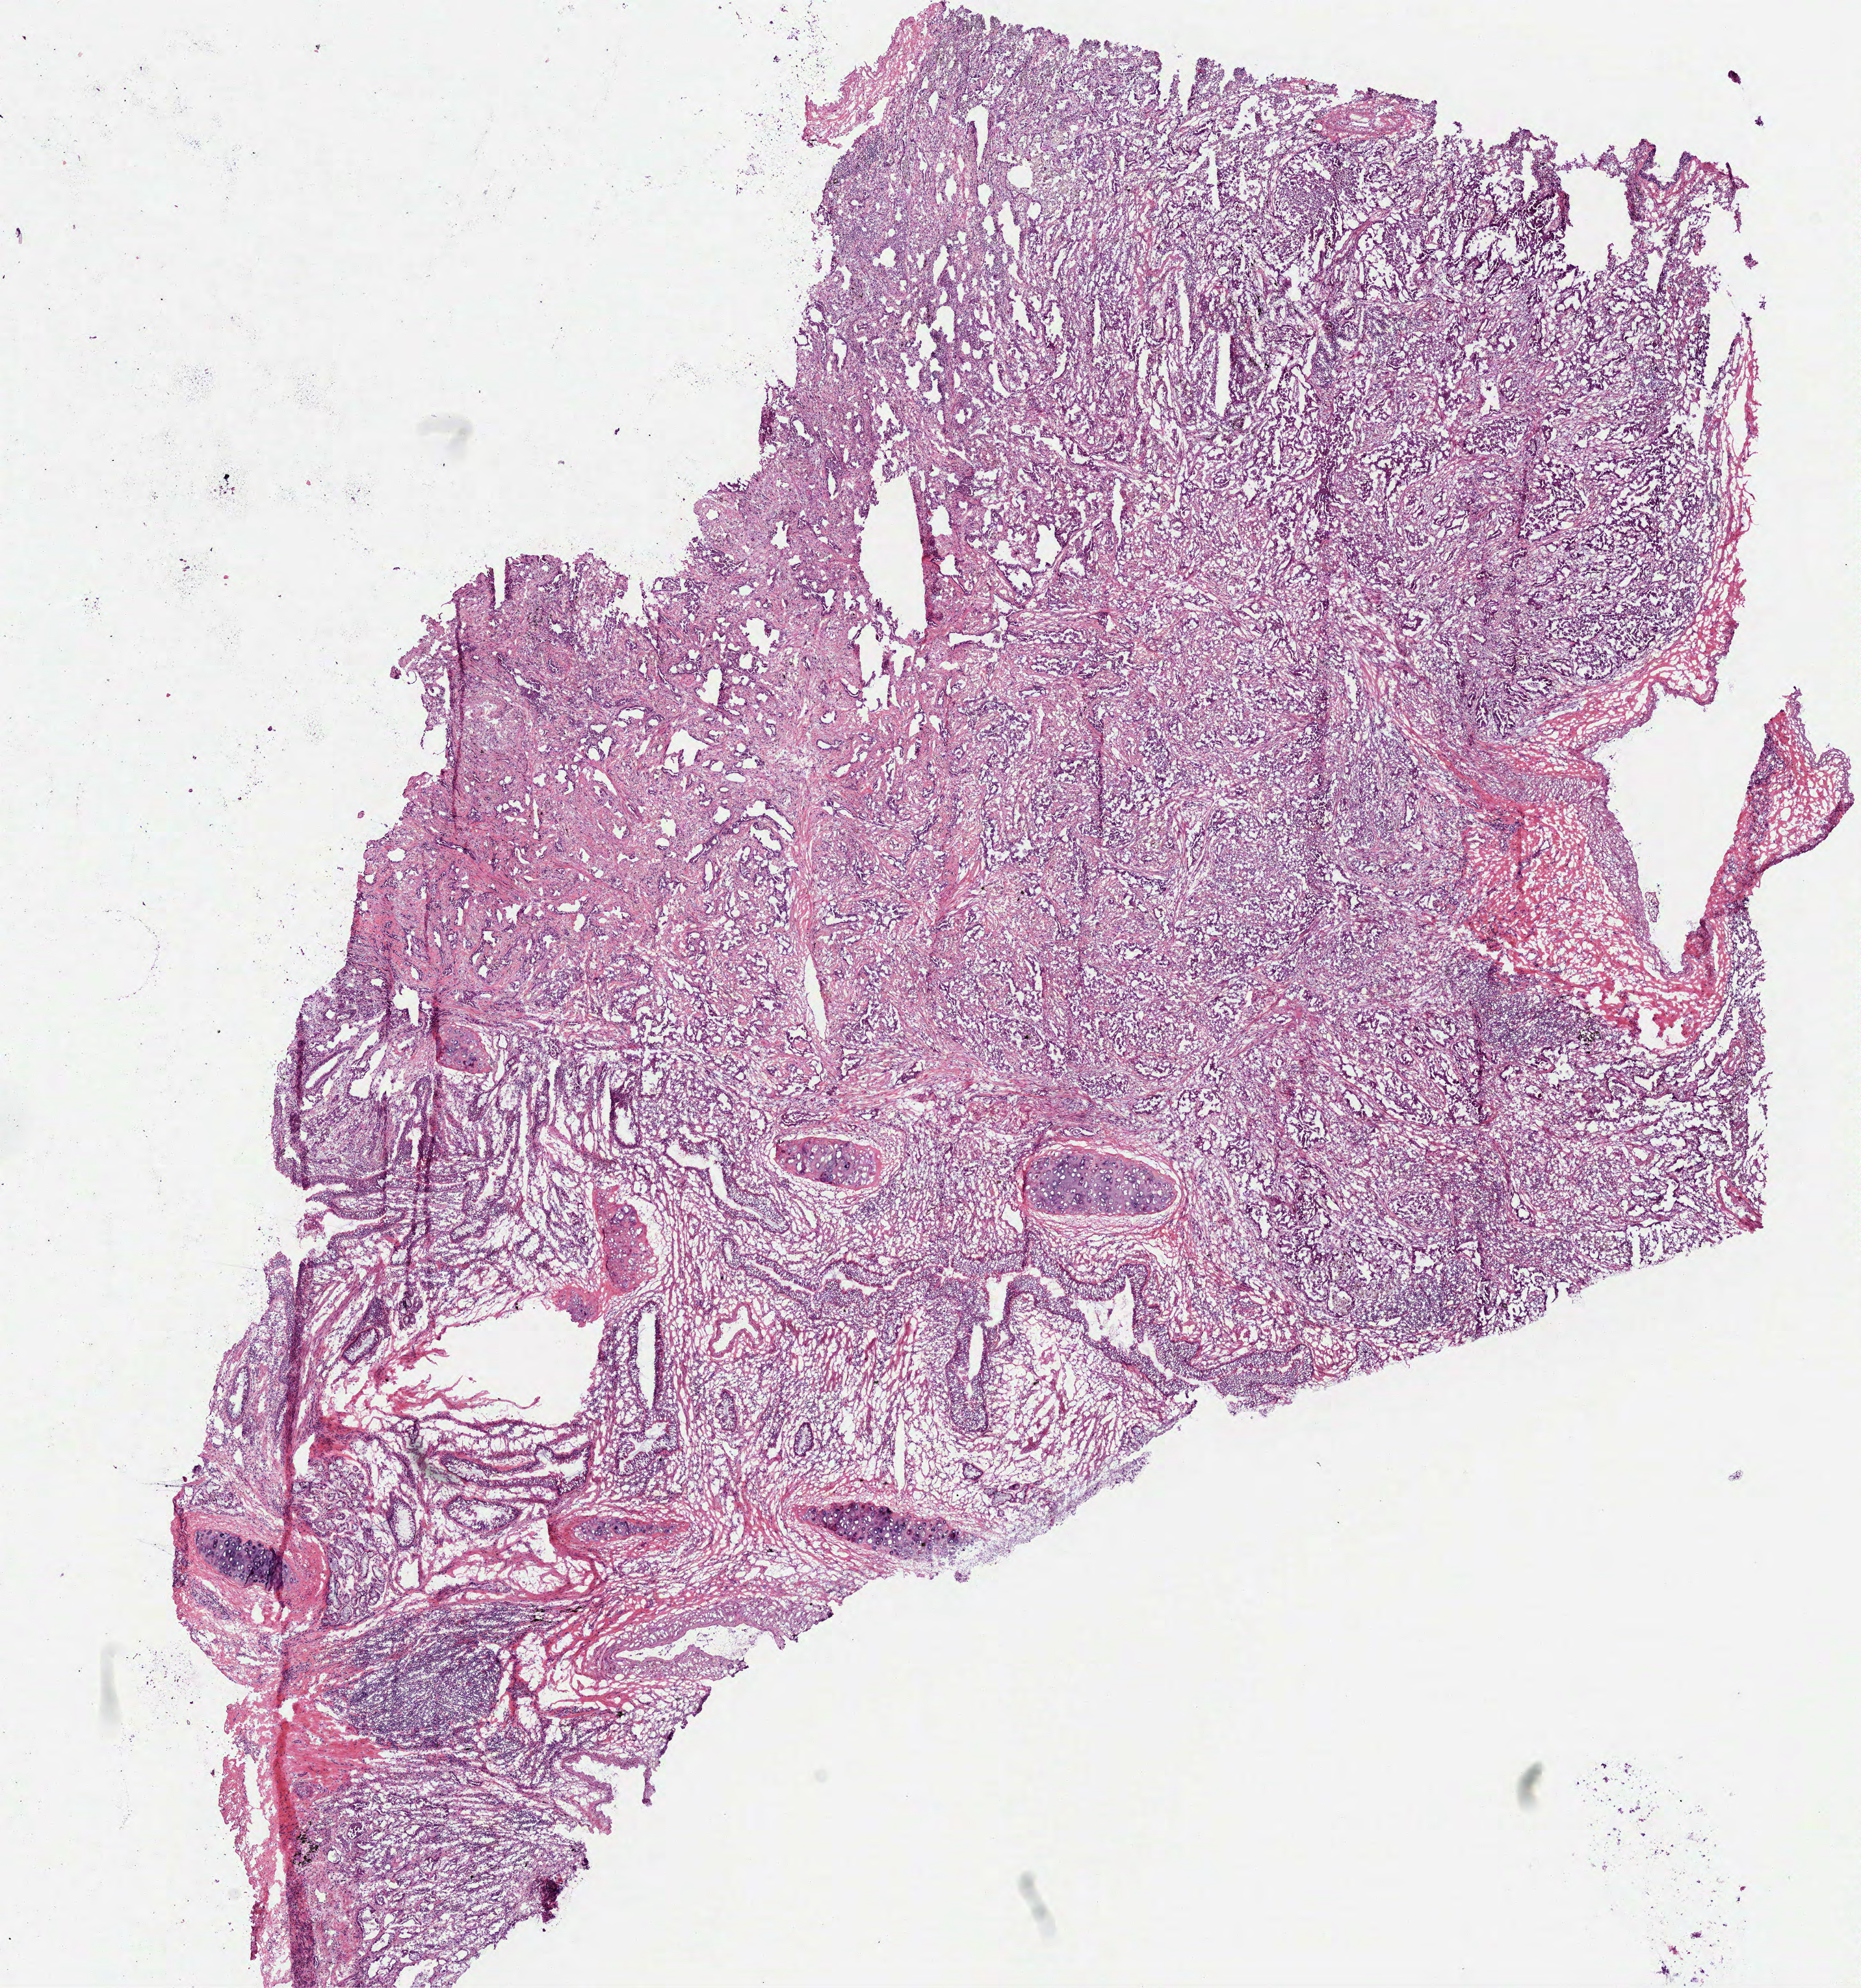
H&E whole-slide image, a low-resolution overview of the entire scanned area, about 11.5 x 12.3 mm (slide scanned at 40x); frozen section from the top of the tissue portion; primary tumour sample from the lung. Female patient; age at initial diagnosis 49 years. Composition of this section per pathologist review: tumour cells 65%, tumour nuclei 75%, normal cells 20%, stromal cells 15%, necrosis 0%.
* AJCC pathologic stage: IIIA
* histologic diagnosis: Adenocarcinoma with mixed subtypes (upper lobe, lung)
* laterality: right